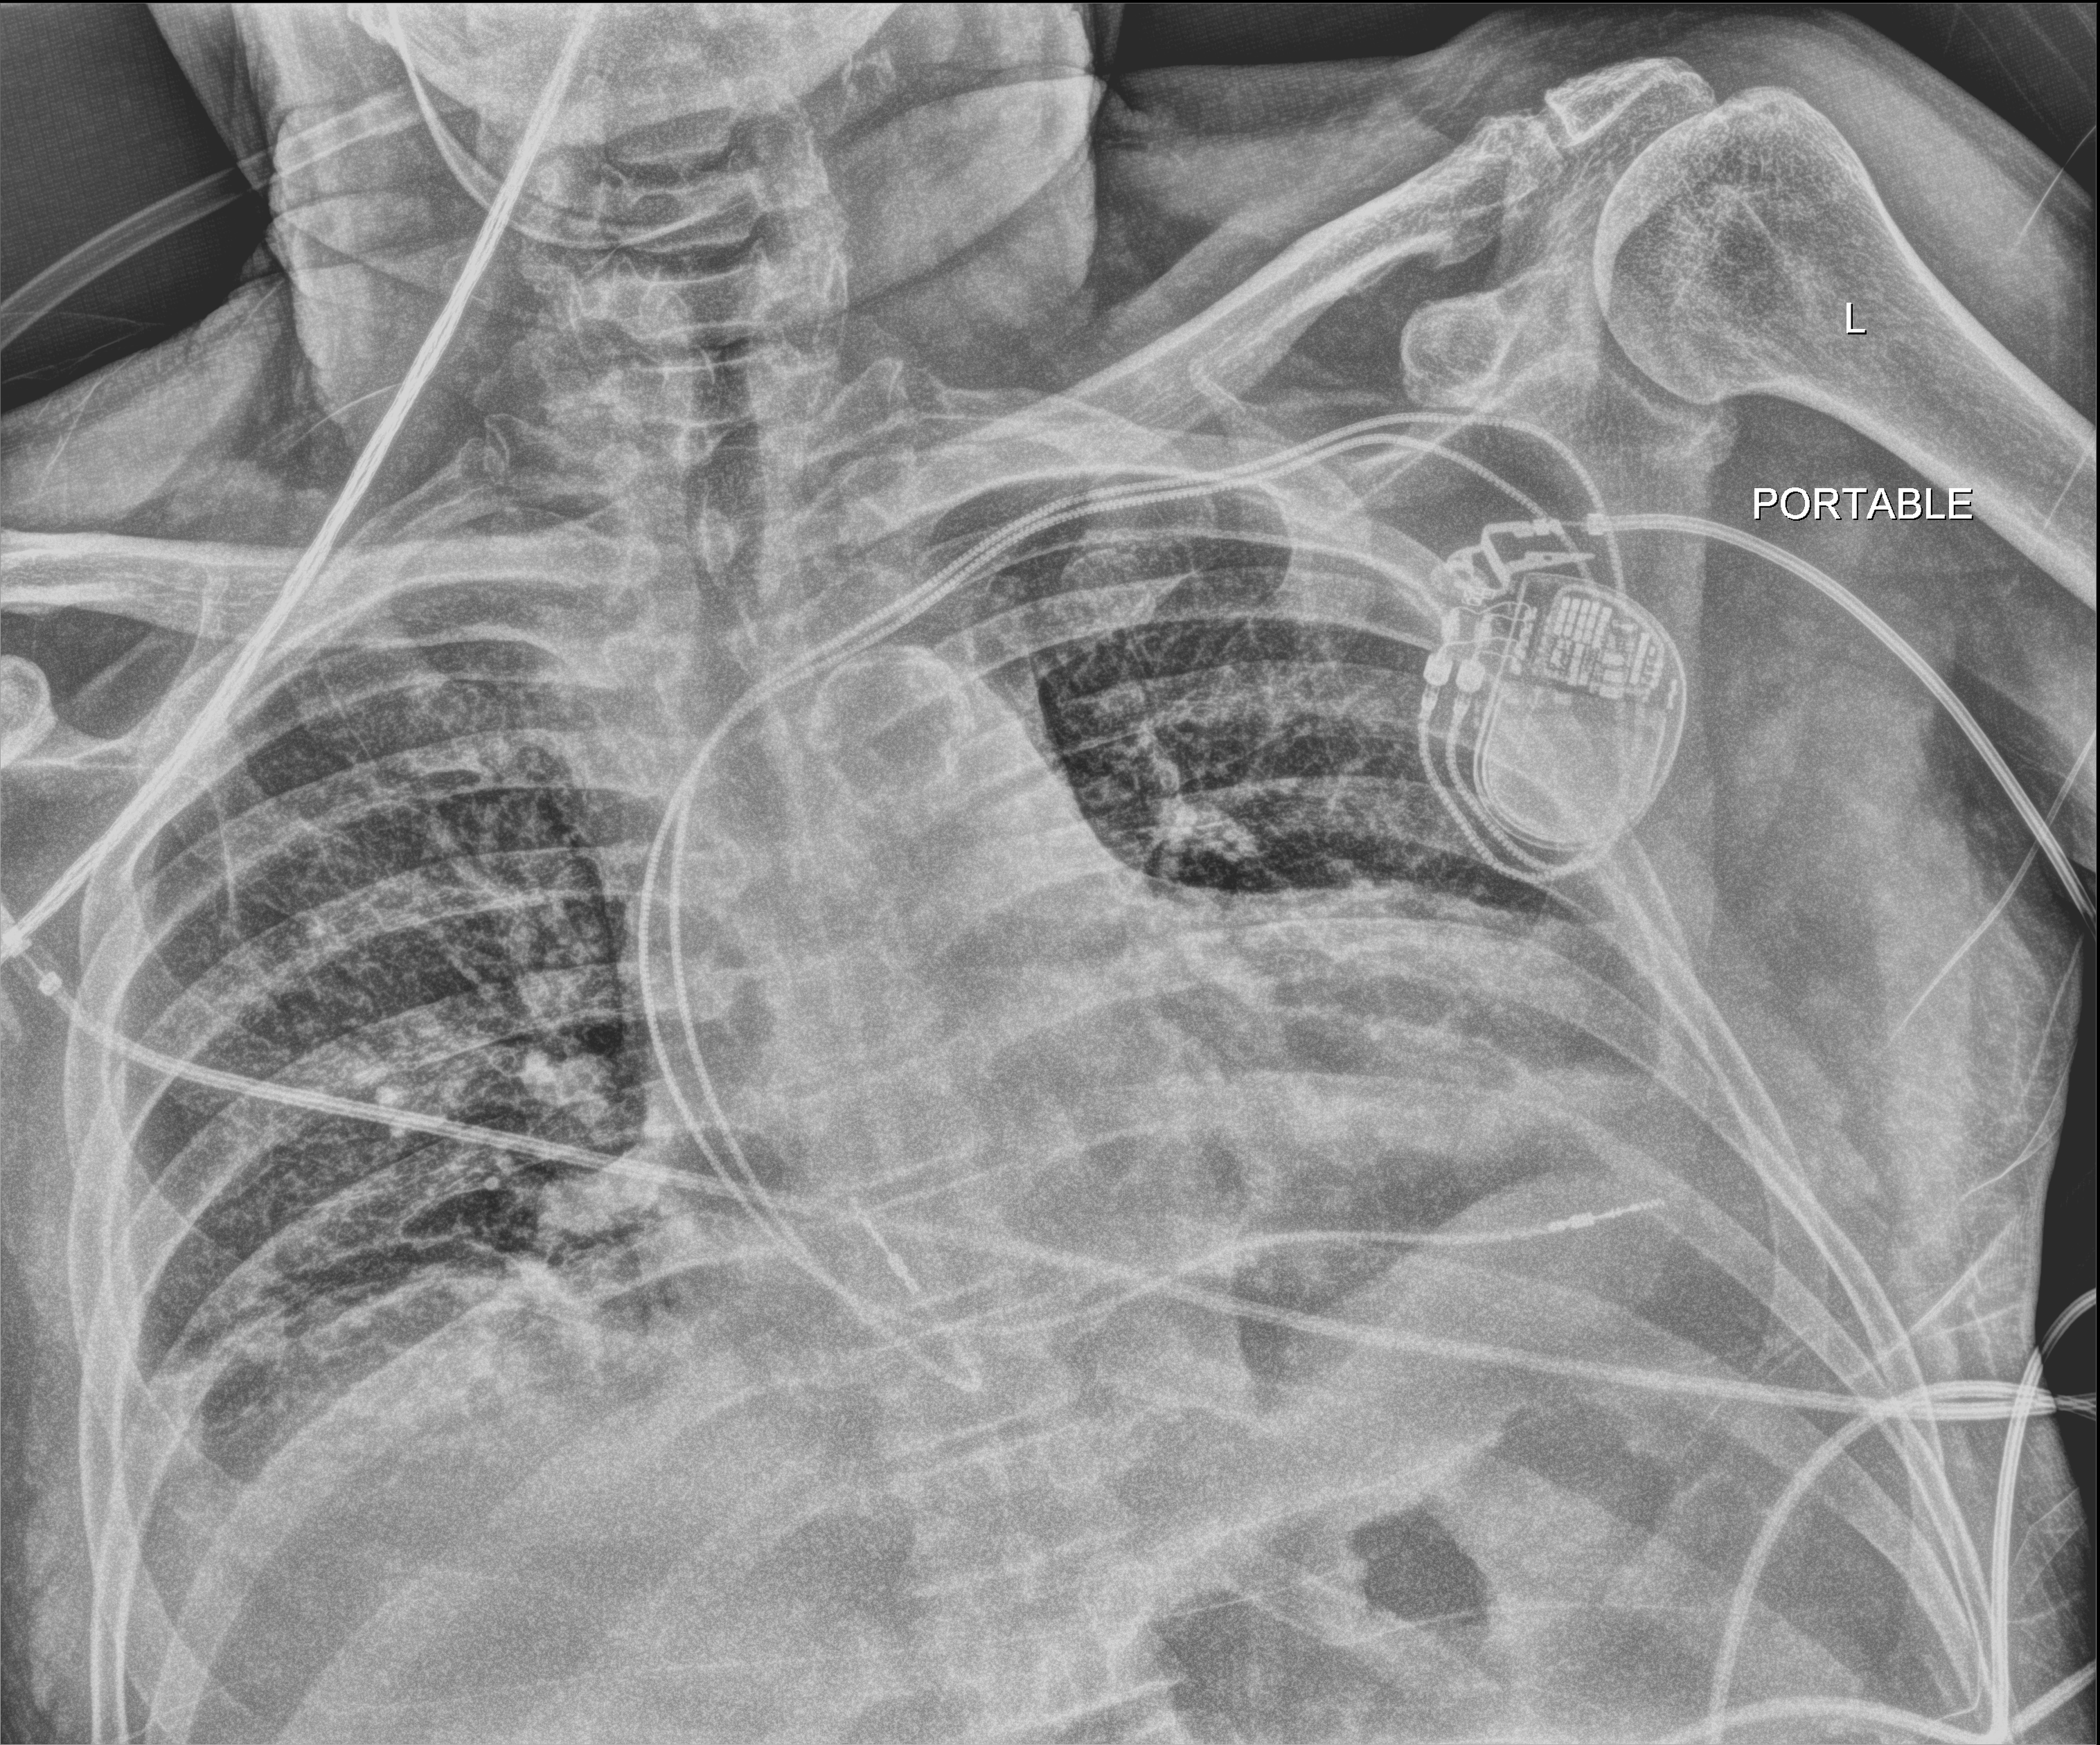
Bedside chest radiograph (digital radiography); anteroposterior (AP) projection. Male patient hospitalised with COVID-19, age 60–74 years.
Admission-level facts for this patient (not findings on this image; timing relative to this image not recorded):
- admitted to intensive care during this hospital stay: yes
- mechanically ventilated during this hospital stay: yes